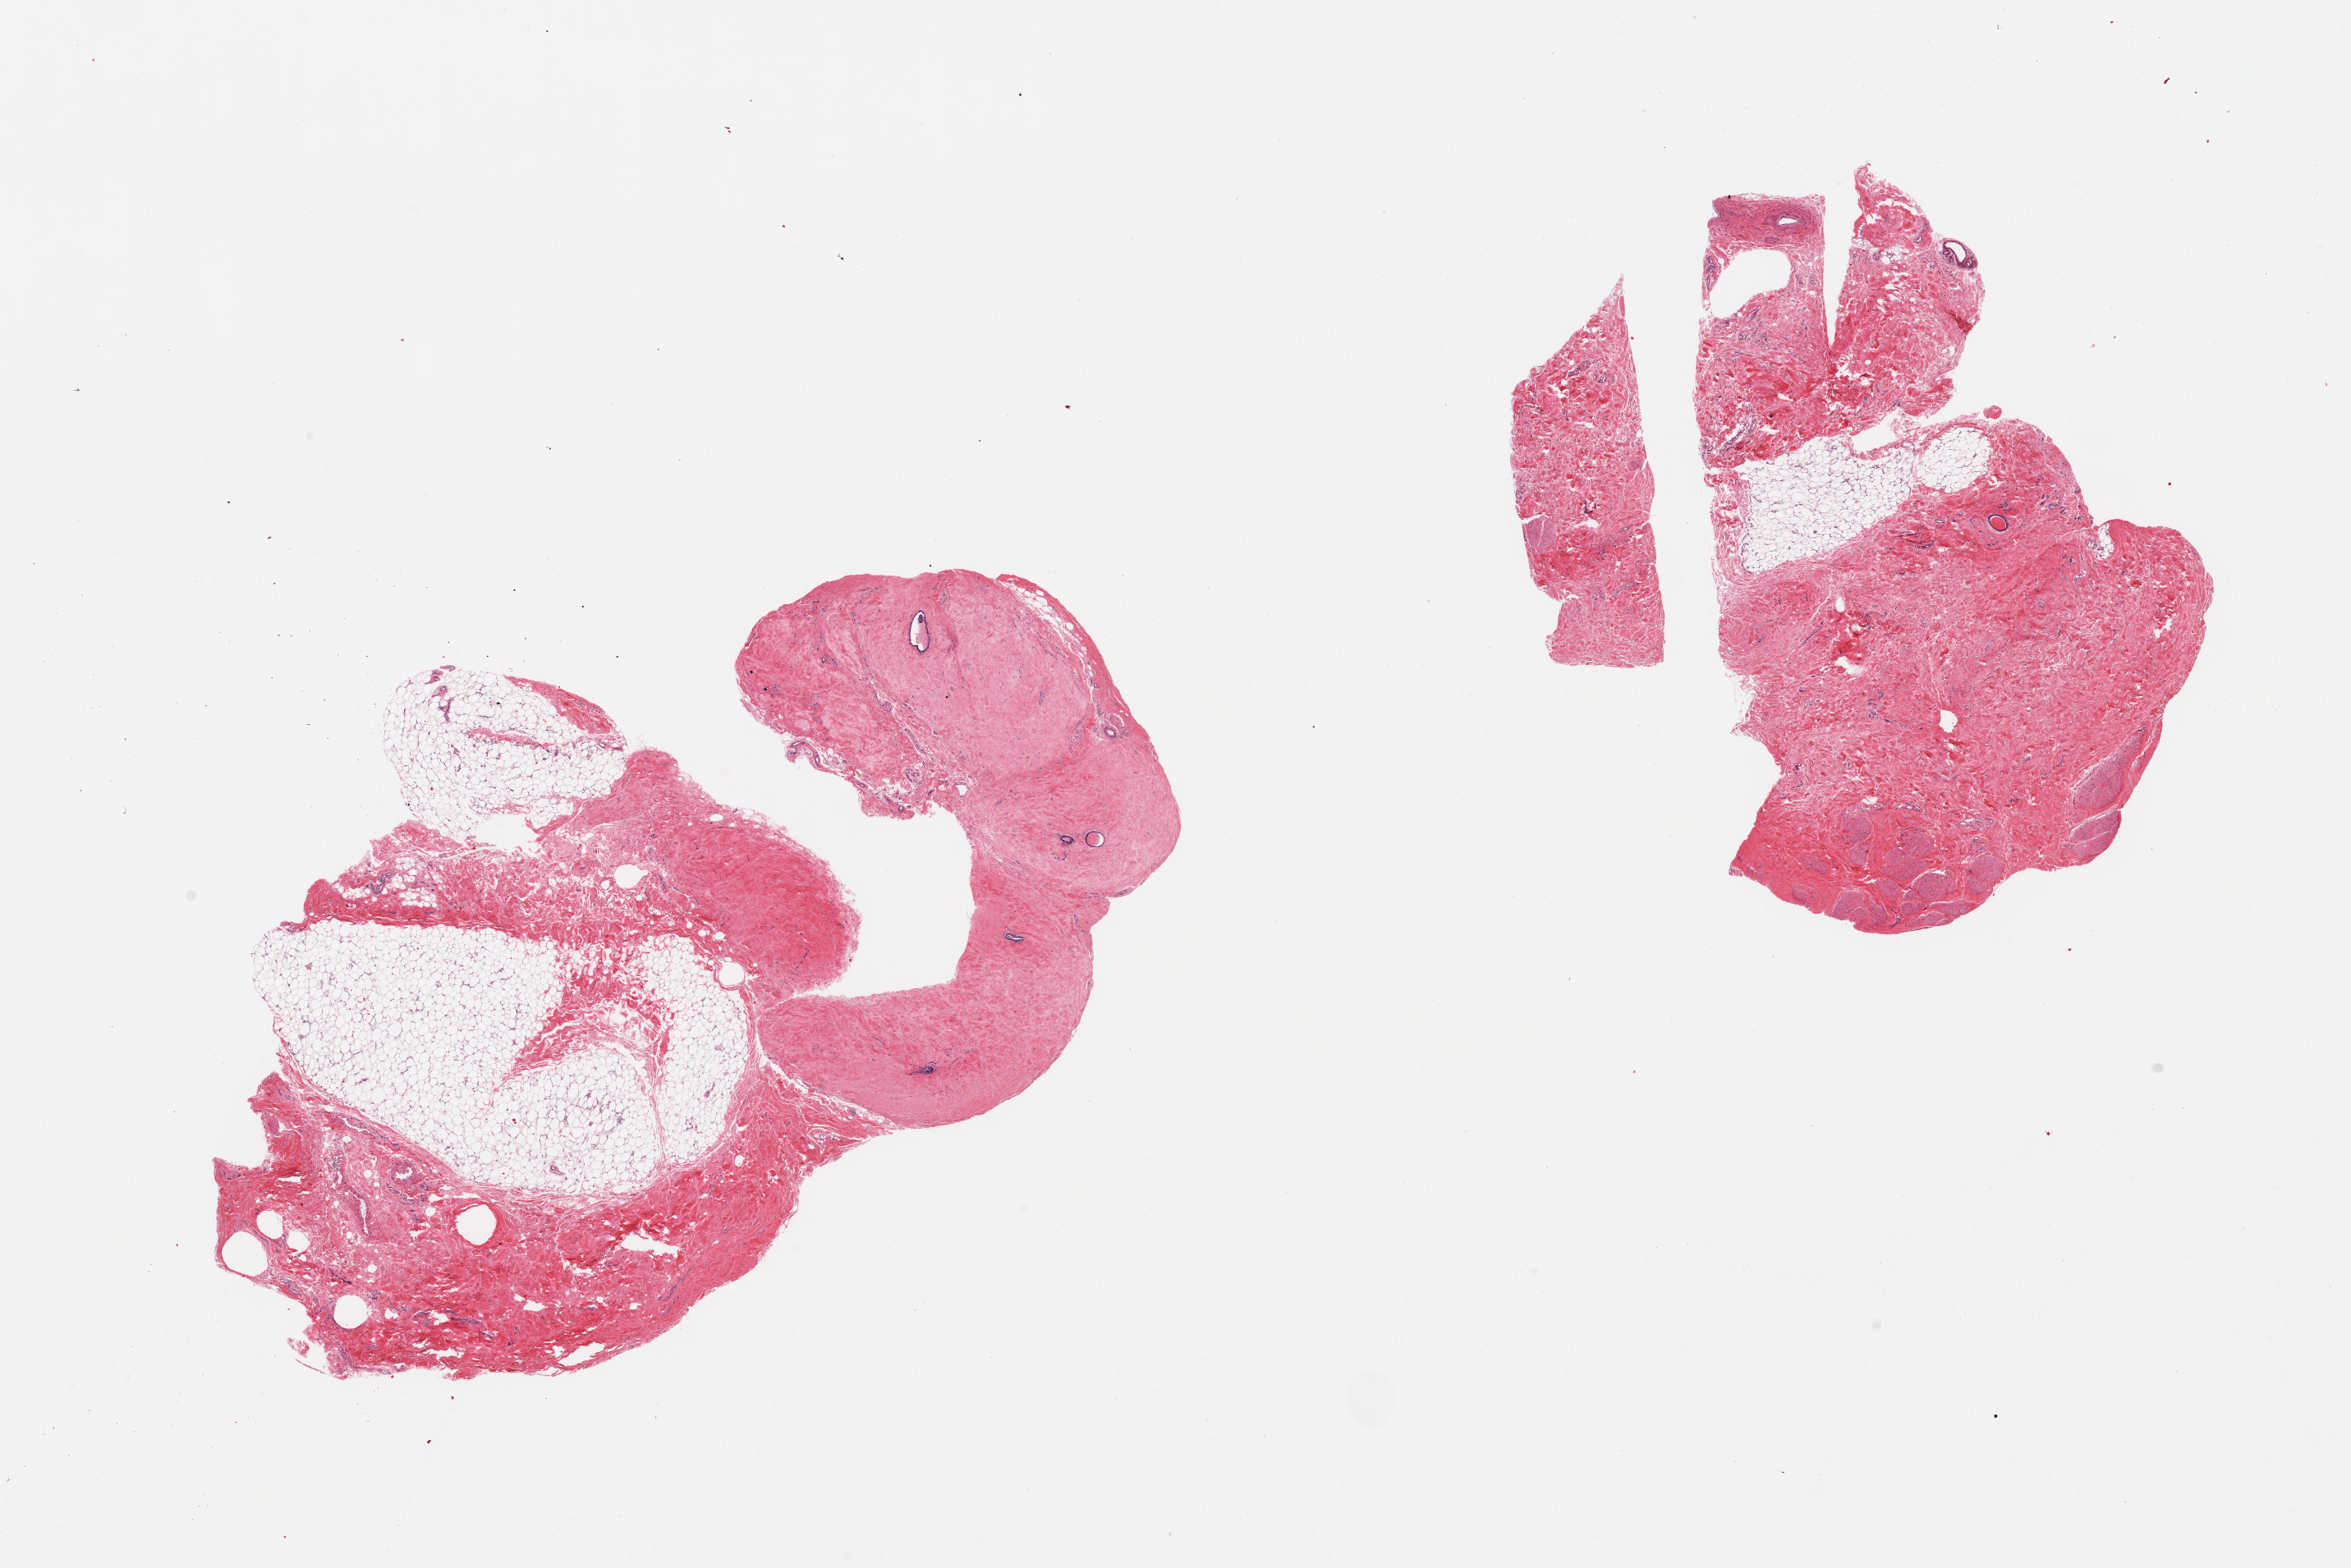
Hematoxylin and eosin (H&E) whole-slide image, whole scanned area (about 22.6 x 15.1 mm) shown as a low-resolution overview, PAXgene-fixed paraffin-embedded (PFPE) section, section of breast (target tissue), tissue donor sample. Donor sex: female.
Review note (as recorded): 2 pieces; atrophic ducts, no lobules; nerves in 1 piece = 10%.